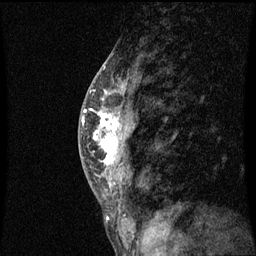
Breast MRI (dynamic contrast-enhanced), one sagittal slice. Dynamic contrast-enhanced series, image 2 of 3 at this slice position (ordered by acquisition). 1.5 T. TE 4.2 ms, TR 8.9 ms. 2 mm slice thickness. 256 × 256 image matrix. Female patient, age 50 years. Case-level facts recorded for this patient, not image findings: setting: breast cancer imaged before/during neoadjuvant chemotherapy; receptor status: triple-negative.
Annotated regions visible in this slice (semi-automatic segmentation, software-assisted and operator-edited):
- analysis volume of interest (the breast-tissue region the enhancement analysis was run in; not a lesion): bounding box [x1, y1, x2, y2] px = [84, 80, 135, 171]
- tumour enhancement mask (voxels above the 70 % enhancement threshold inside the analysis volume of interest): [84, 110, 121, 167]